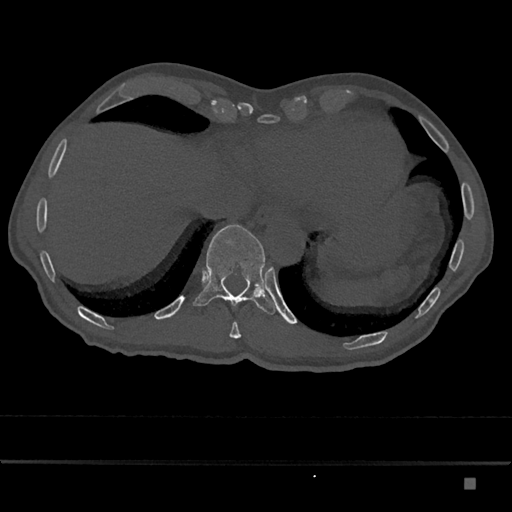
CT including the spine, one axial slice; position 691 of 797 along the scan axis; reconstruction kernel Br40s/3; bone window (W 1800 / L 400 HU); 0.5 mm slice thickness; 512 × 512 image matrix. Patient: male, 72 years. Case-level facts recorded for this patient, not image findings: primary cancer: prostate.
Annotated regions visible in this slice (semi-automatic segmentation, software-assisted and operator-edited):
- T10 vertebra: bounding box <229,322,241,339> (left, top, right, bottom; pixels)
- T11 vertebra: <193,224,276,315>